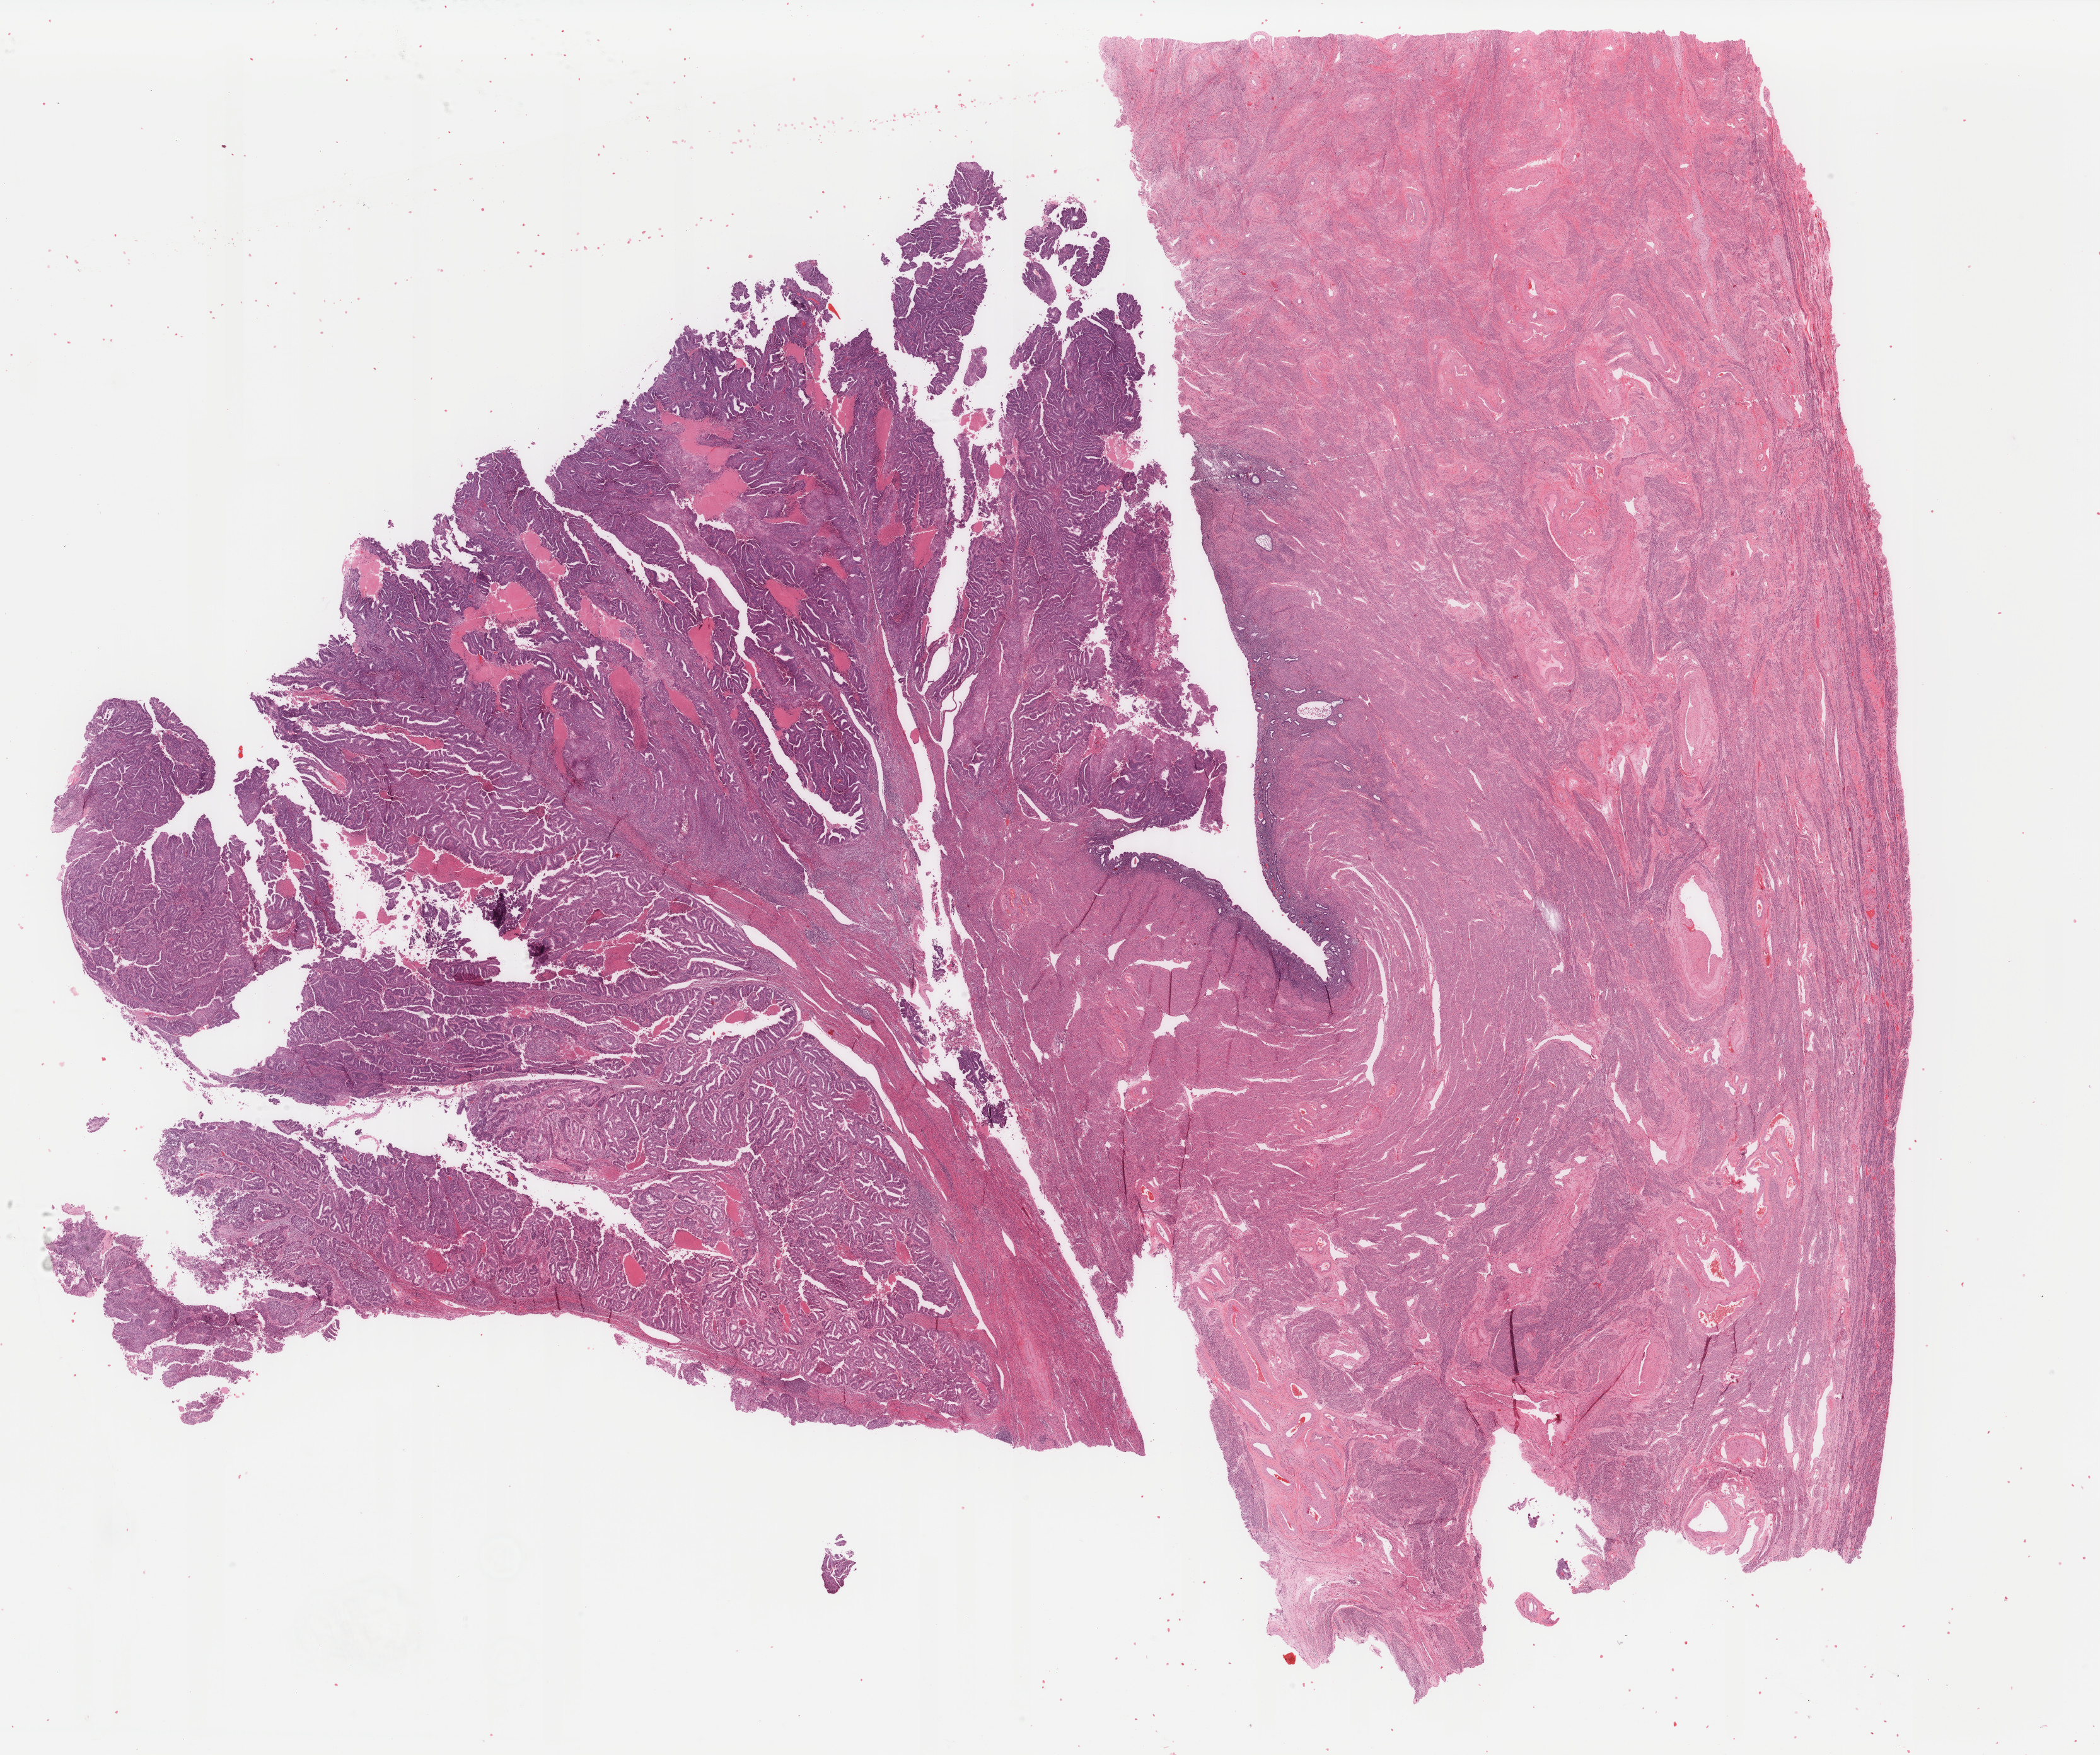
Digitized H&E tissue section (whole slide), low-resolution overview of the scanned area, about 26.4 x 22.1 mm (from a 40x scan), formalin-fixed paraffin-embedded (FFPE) diagnostic section, primary tumour sample from the uterus. Female patient; age at initial diagnosis 47 years. Histologic grade: G2 (moderately differentiated).
- lymph nodes positive (case pathology): 0 of 3 examined
- pathologic diagnosis: Endometrioid adenocarcinoma, NOS
- FIGO stage: IB